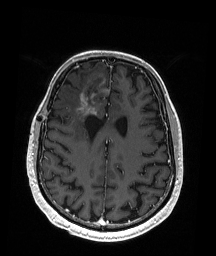
Brain MRI from a brain-tumour surgery series, one axial slice. Position 68 of 192 along the scan axis. T1-weighted post-contrast. 1 mm slice thickness. 216 × 256 image matrix, field of view 211 × 250 mm. Case-level facts recorded for this patient, not image findings: histopathology: Astrocytoma; WHO grade: 3; IDH mutation: yes; tumour location: Right Frontal.
Outlined on this slice (manually delineated by an expert):
- tumour: box from (x=79, y=93) to (x=97, y=117) px